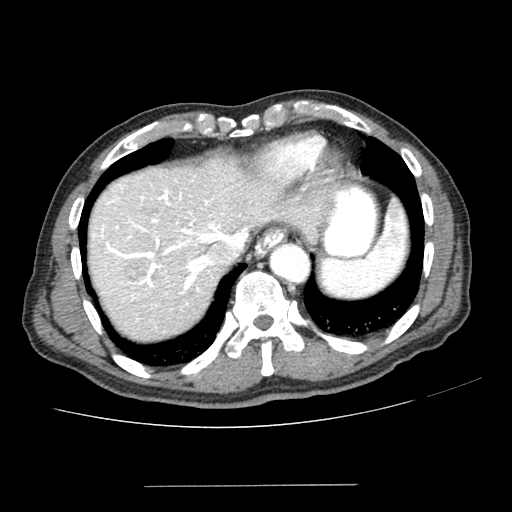
Contrast-enhanced abdominal CT (liver protocol), one axial slice; reconstruction kernel SOFT; 100 kVp; one of 2 acquisitions stored at this slice position; soft-tissue window (W 400 / L 40 HU); 2.5 mm slice thickness; 512 × 512 image matrix. Case-level facts recorded for this patient, not image findings: diagnosis: hepatocellular carcinoma (patient treated with transarterial chemoembolisation; whether this scan precedes or follows treatment is not stated here); TNM stage (as recorded): Stage-I; Child-Pugh class: A; tumour differentiation: poorly differentiated; tumour size: 1.6 cm.
Annotated regions visible in this slice (semi-automatically segmented with operator editing):
- liver parenchyma outside the tumour (the mass and vessels are separate outlines, so this box may not span the whole liver): bounding box (x1, y1, x2, y2) in pixels: (88, 158, 331, 340)
- mass: (123, 257, 150, 282)
- liver vessels: (99, 185, 246, 300)